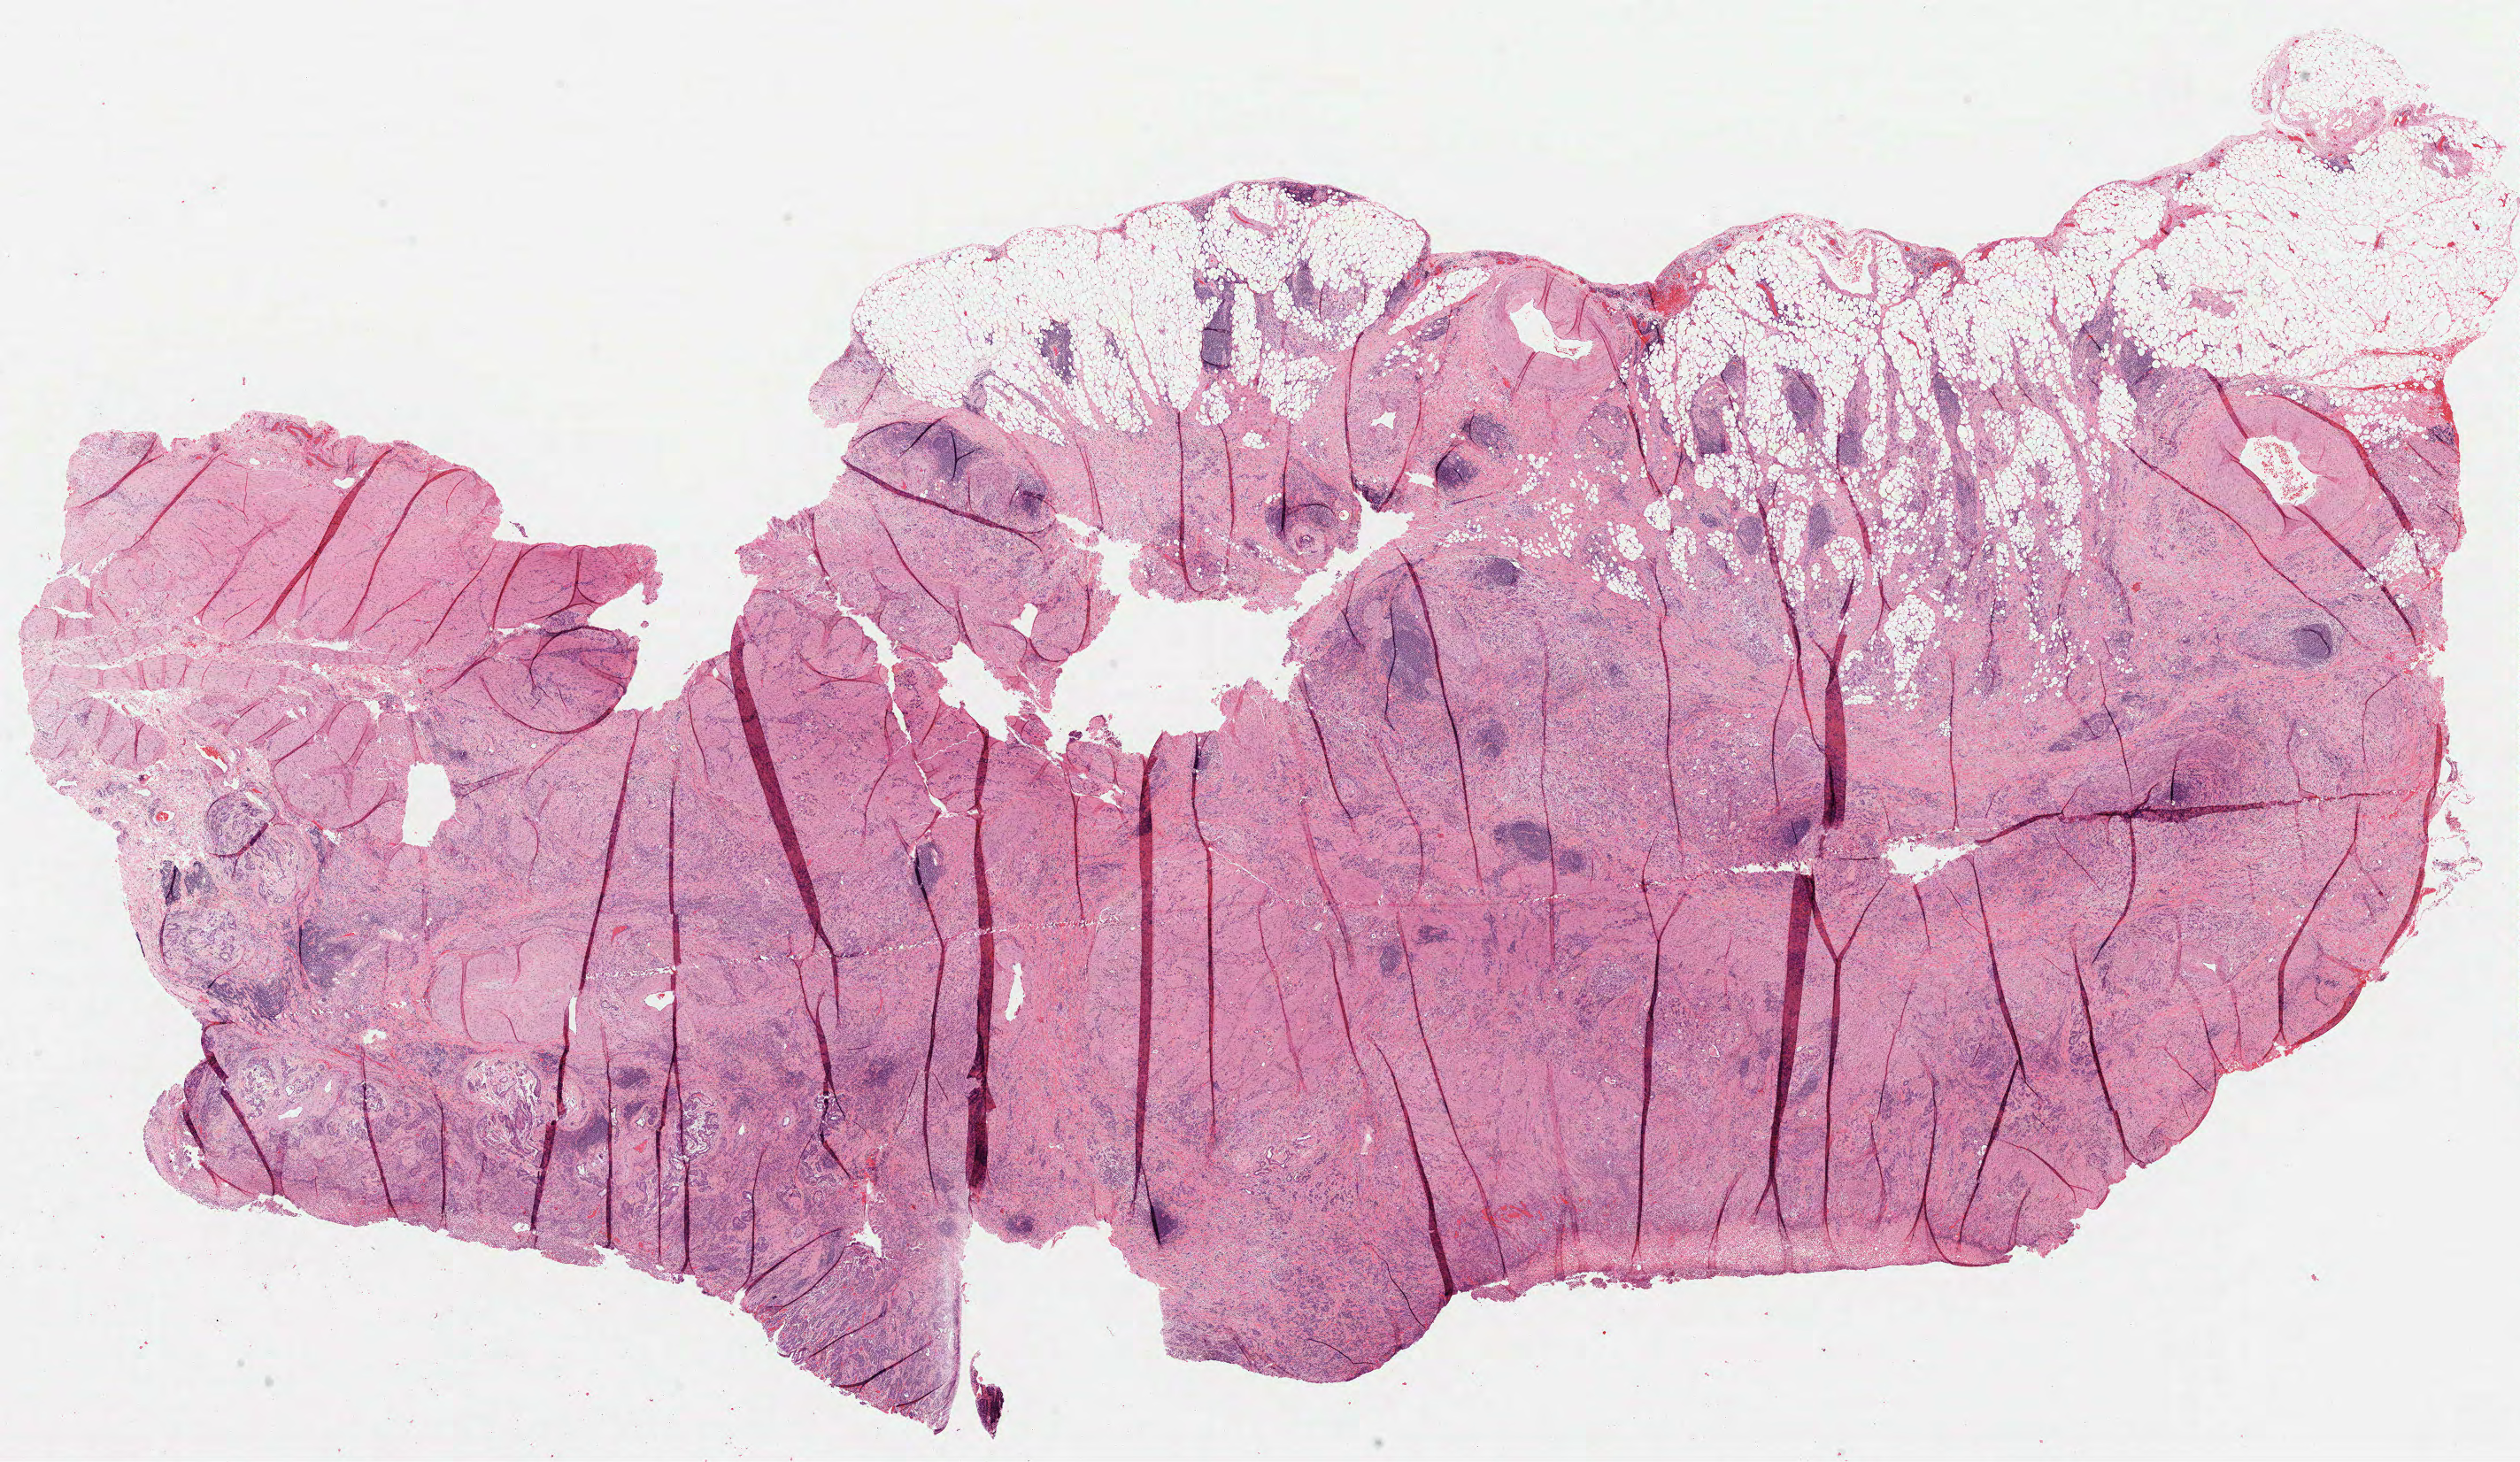
Whole-slide histology image, H&E-stained, low-resolution overview of the scanned area, about 23.0 x 13.3 mm, FFPE section, sample: primary tumour, stomach. Male patient; age at initial diagnosis 69 years. Histologic grade: G3 (poorly differentiated).
* histologic diagnosis: Adenocarcinoma, NOS (body of stomach)
* AJCC pathologic stage: IIA (7th edition)
* lymph nodes positive (case pathology): 0 of 15 examined